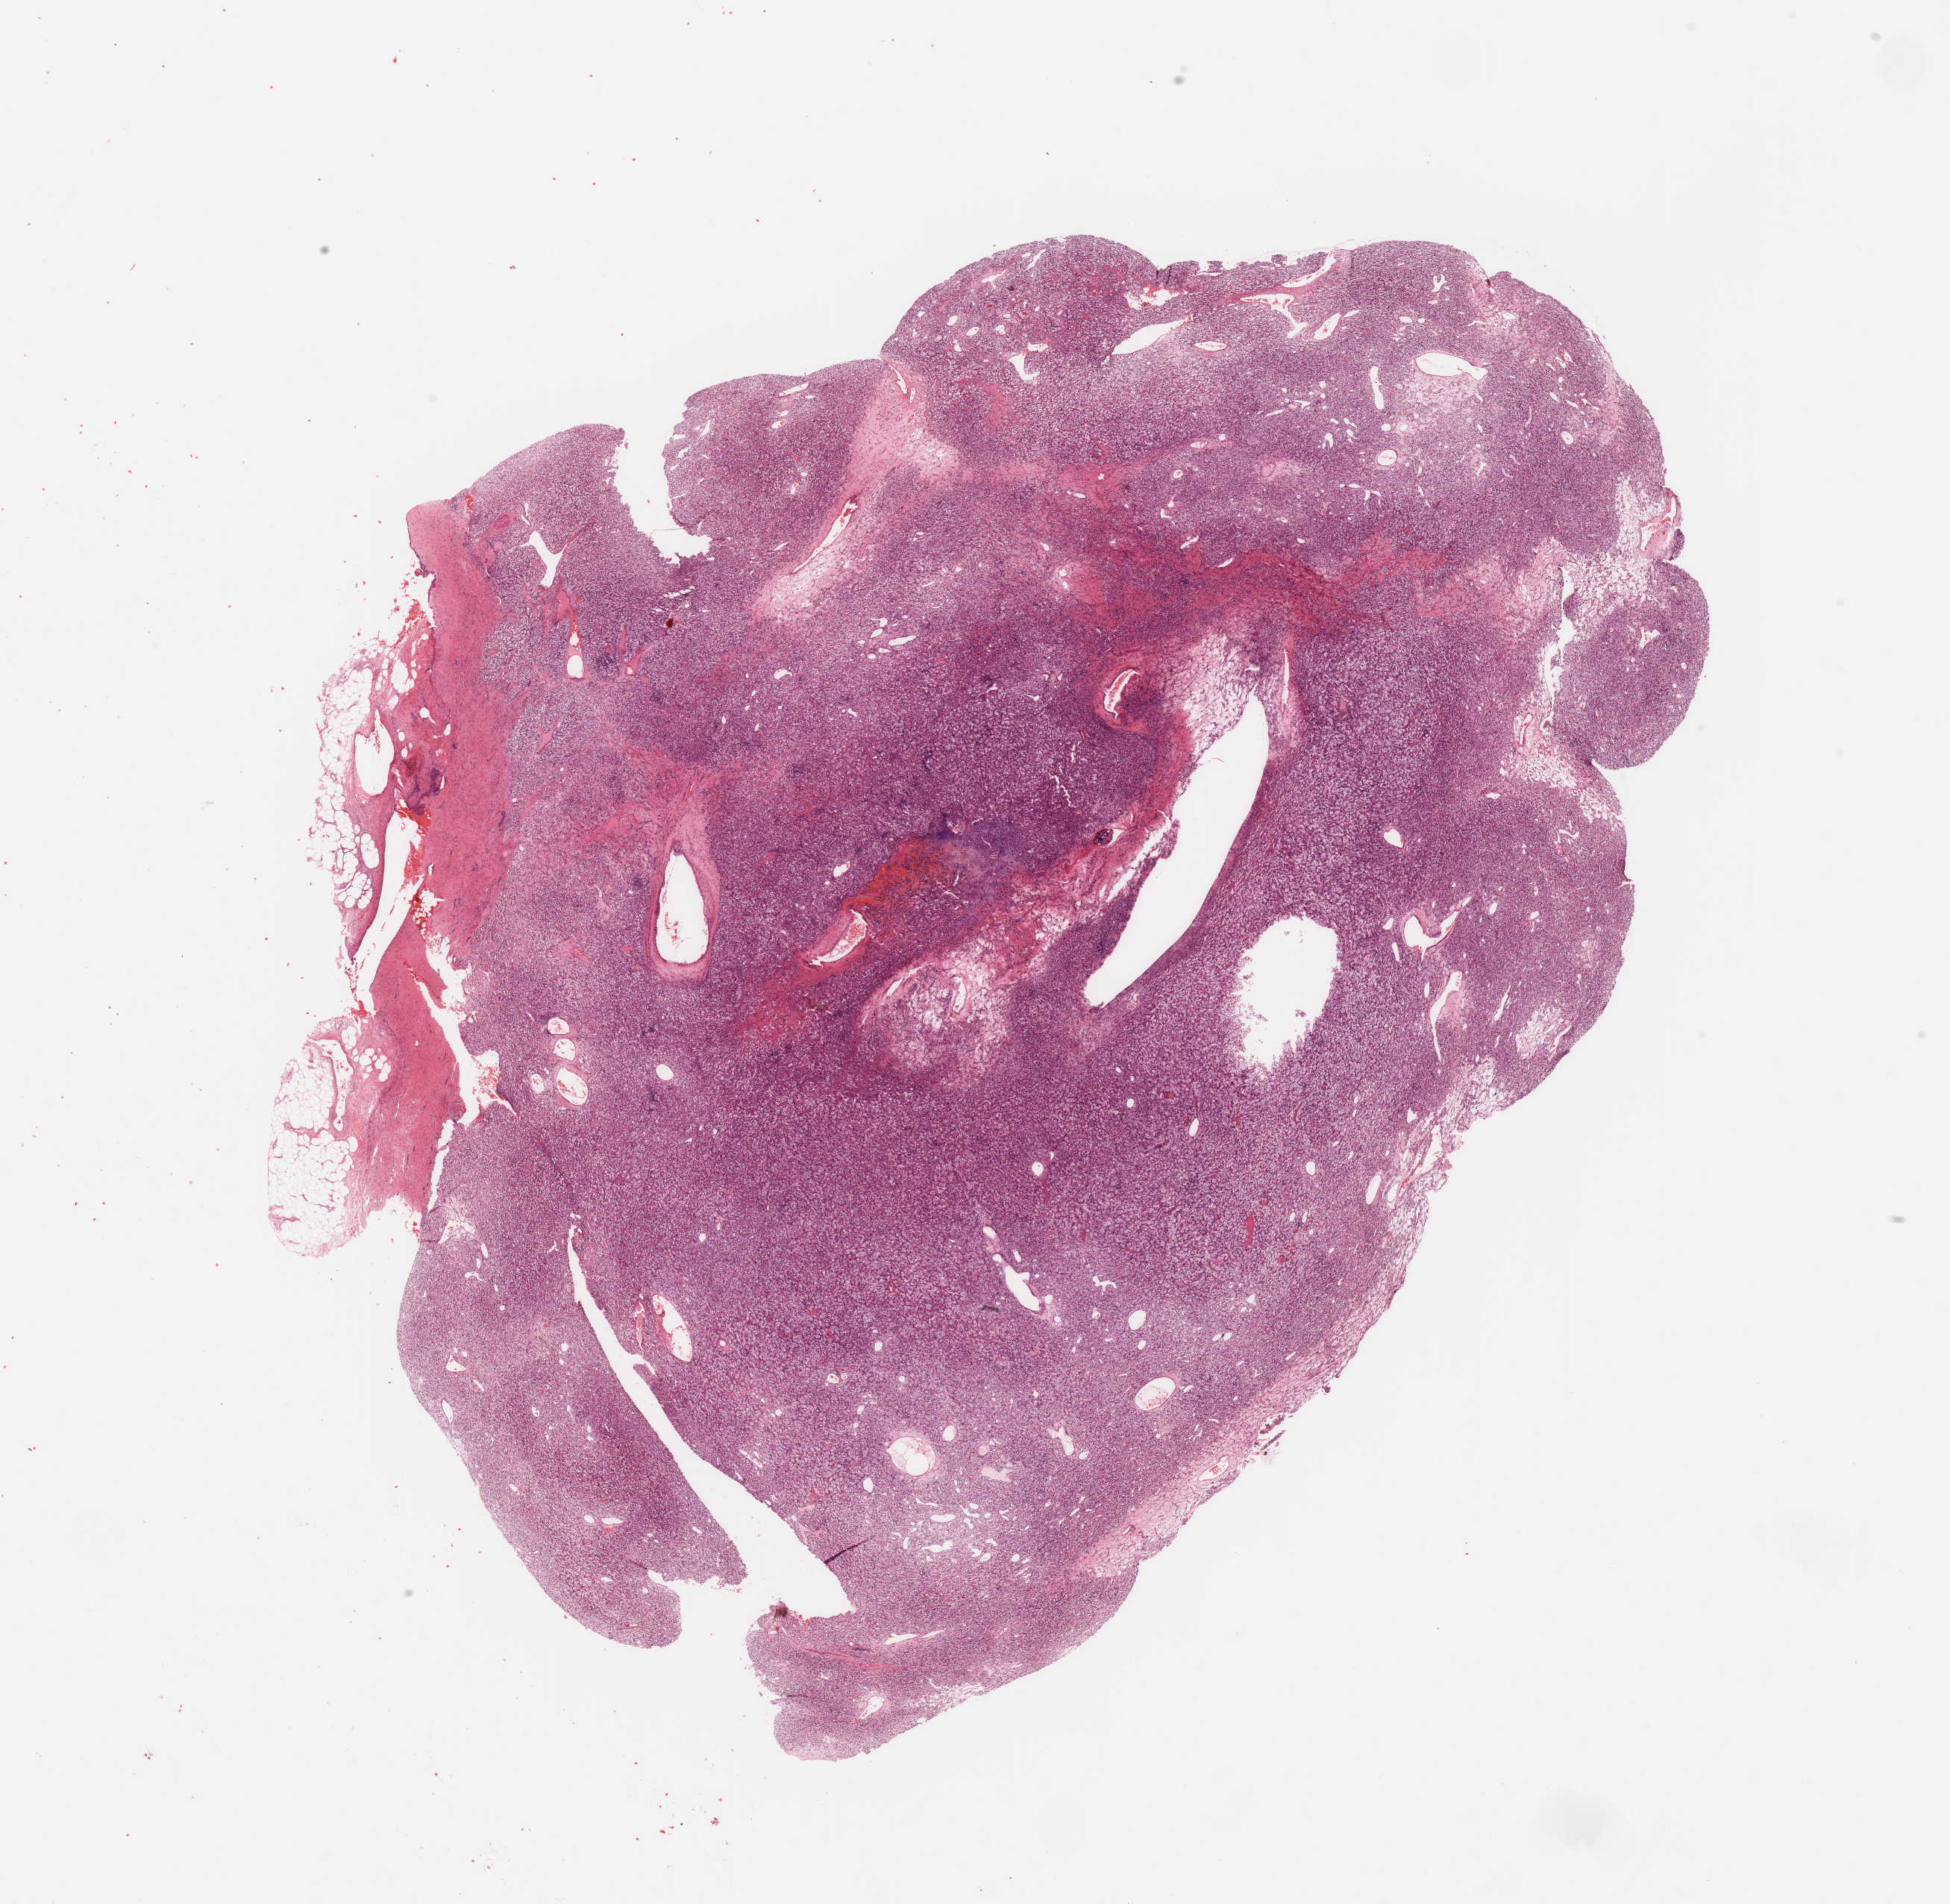
Whole-slide histology image, H&E, low-resolution overview of the scanned area, about 20.7 x 20.2 mm (slide scanned at 20x). Tumour tissue sample, sampled site: kidney. Male, 63 y/o. Histologic grade: G1 (well differentiated). Pathologist review of this section (percent, as recorded): tumour nuclei 85%, necrosis 10%.
Histologic diagnosis: Renal cell carcinoma, NOS.